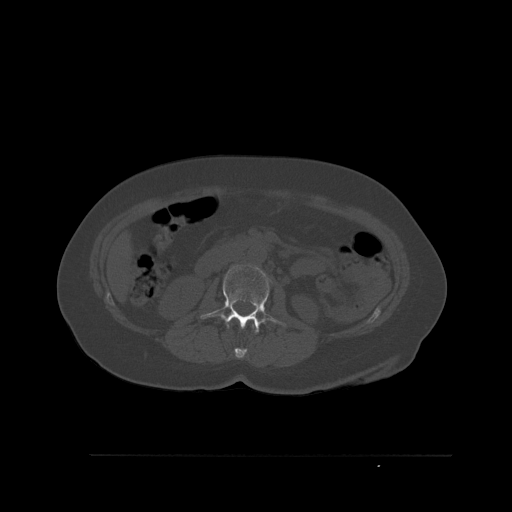
CT including the spine, one axial slice; position 246 of 527 along the scan axis; bone window (W 1800 / L 400 HU); 1.5 mm slice thickness; 512 × 512 image matrix. Female patient, age 73 years. From the clinical record (not read from this slice): primary cancer: breast; vertebrae with lytic lesions (as recorded): L2.
Structures marked on this image (semi-automatic segmentation, software-assisted and operator-edited):
- L1 vertebra: bounding box (x1, y1, x2, y2) in pixels: (234, 324, 254, 359)
- L2 vertebra: (200, 264, 286, 334)